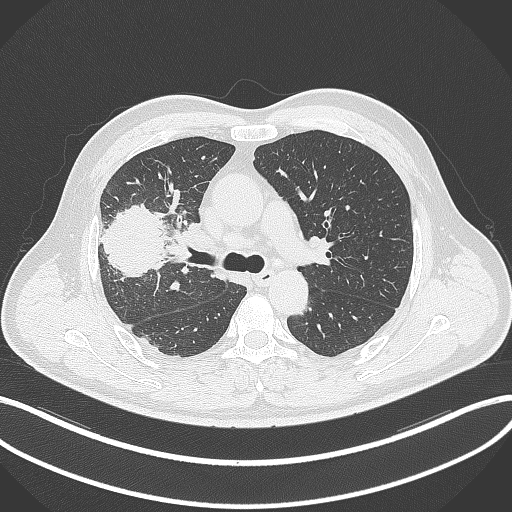
Chest CT, one axial slice; slice 215 of 348 in the series (ordered by position); lung window (W 1500 / L -600 HU); 1 mm slice thickness; 512 × 512 image matrix. Male patient, age 55 years. Case-level facts recorded for this patient, not image findings: clinical TNM (as recorded): T3 N2 M1.
Annotated regions visible in this slice (bounding box drawn by a radiologist):
- lung tumour (recorded histology: adenocarcinoma): bounding box [x1, y1, x2, y2] px = [95, 201, 170, 281]